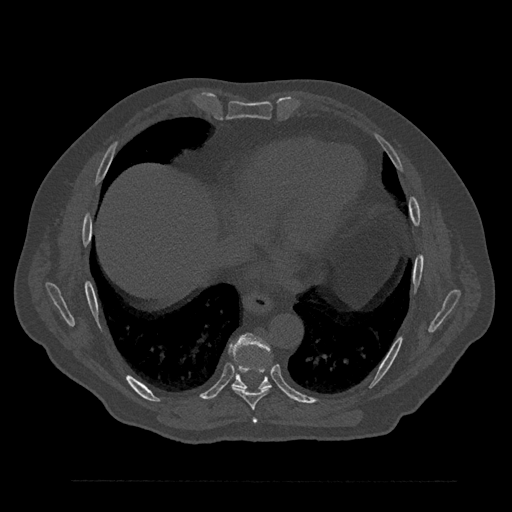
CT including the spine, one axial slice; position 435 of 797 along the scan axis; 120 kVp; bone window (W 1800 / L 400 HU); 0.5 mm slice thickness; 512 × 512 image matrix. Male patient, age 61 years. From the clinical record (not read from this slice): primary cancer: prostate.
Outlined on this slice (semi-automatically segmented with operator editing):
- T7 vertebra: bounding box <253,418,257,424> (left, top, right, bottom; pixels)
- T8 vertebra: <231,367,272,410>
- T9 vertebra: <230,334,272,389>